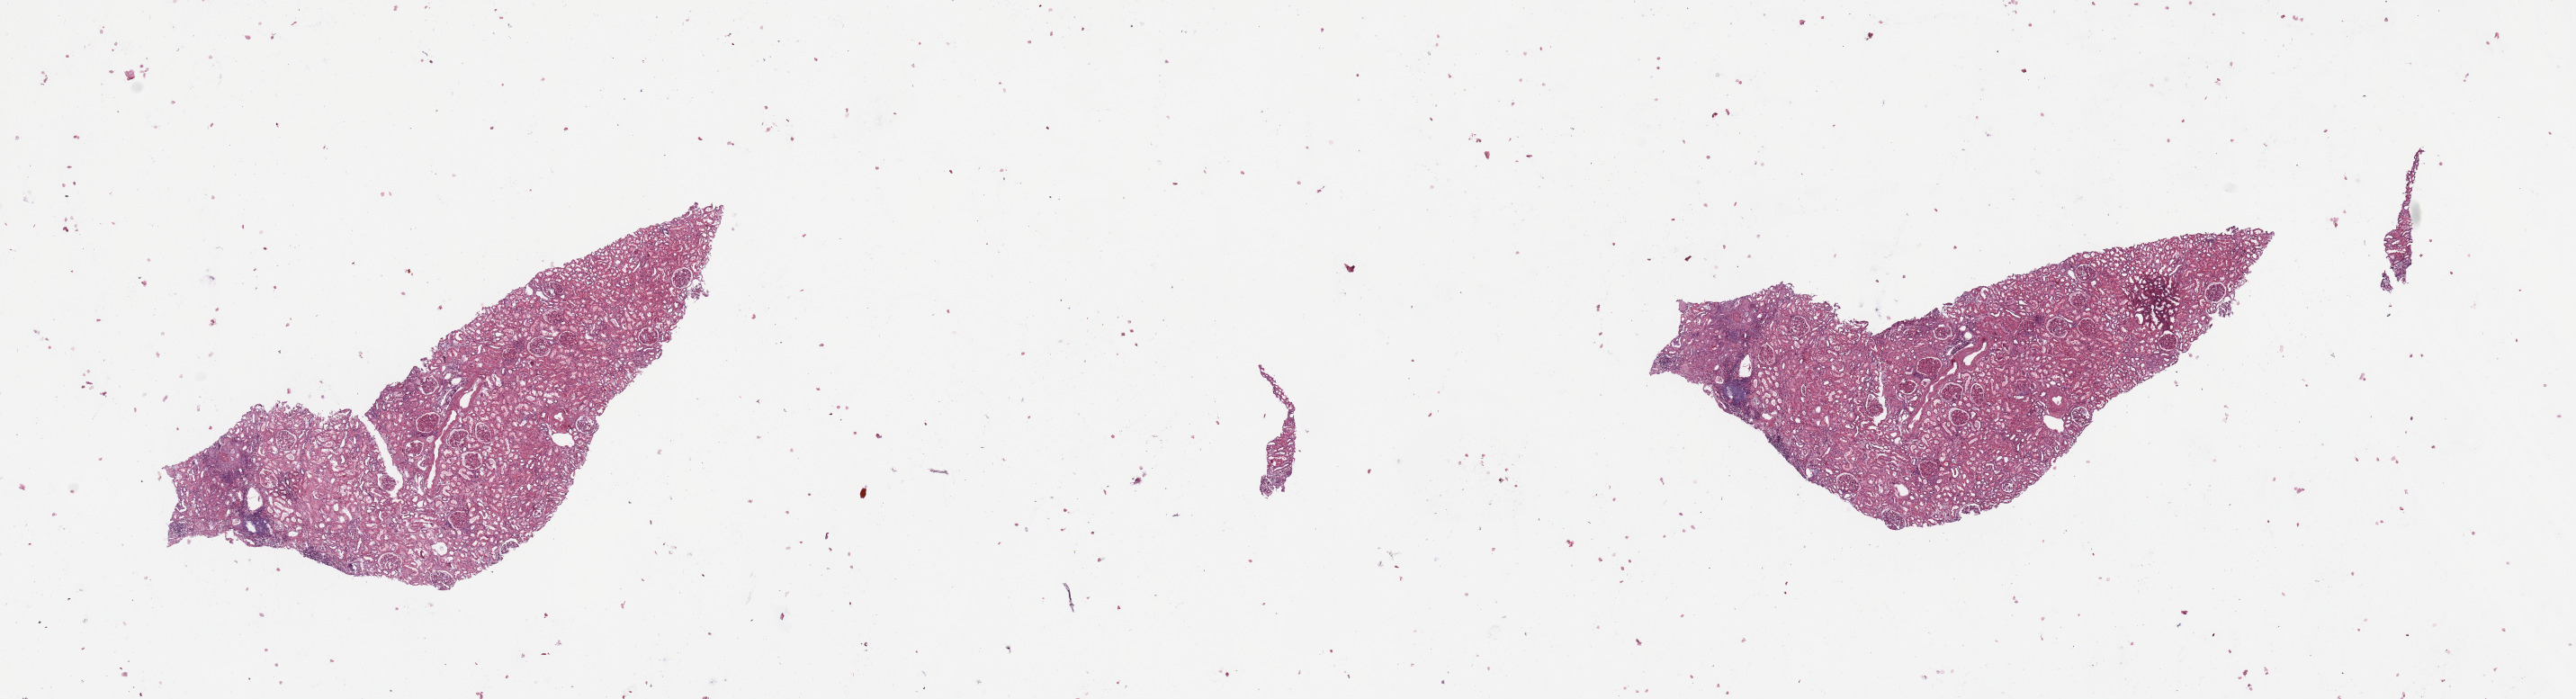
Whole-slide histology image, Hematoxylin and eosin (H&E) stained, whole scanned area (about 22.6 x 6.1 mm, acquisition: 20x scan) shown as a low-resolution overview, normal (non-tumour) tissue sample, sampled site: kidney. Patient: male, age 69 years.
This section: normal (non-tumour) tissue from the same patient. Patient diagnosis: Renal cell carcinoma, NOS.